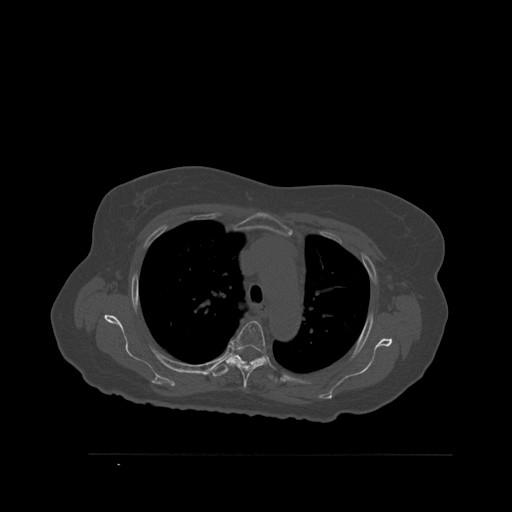
CT including the spine, one axial slice. Position 404 of 527 along the scan axis. Bone window (W 1800 / L 400 HU). 512 × 512 image matrix, field of view 470 × 470 mm. Female patient, age 73 years. Case-level facts recorded for this patient, not image findings: primary cancer: breast.
Outlined on this slice (semi-automatically segmented with operator editing):
- T4 vertebra: bounding box (x1, y1, x2, y2) in pixels: (228, 321, 269, 390)
- T5 vertebra: (210, 350, 278, 383)